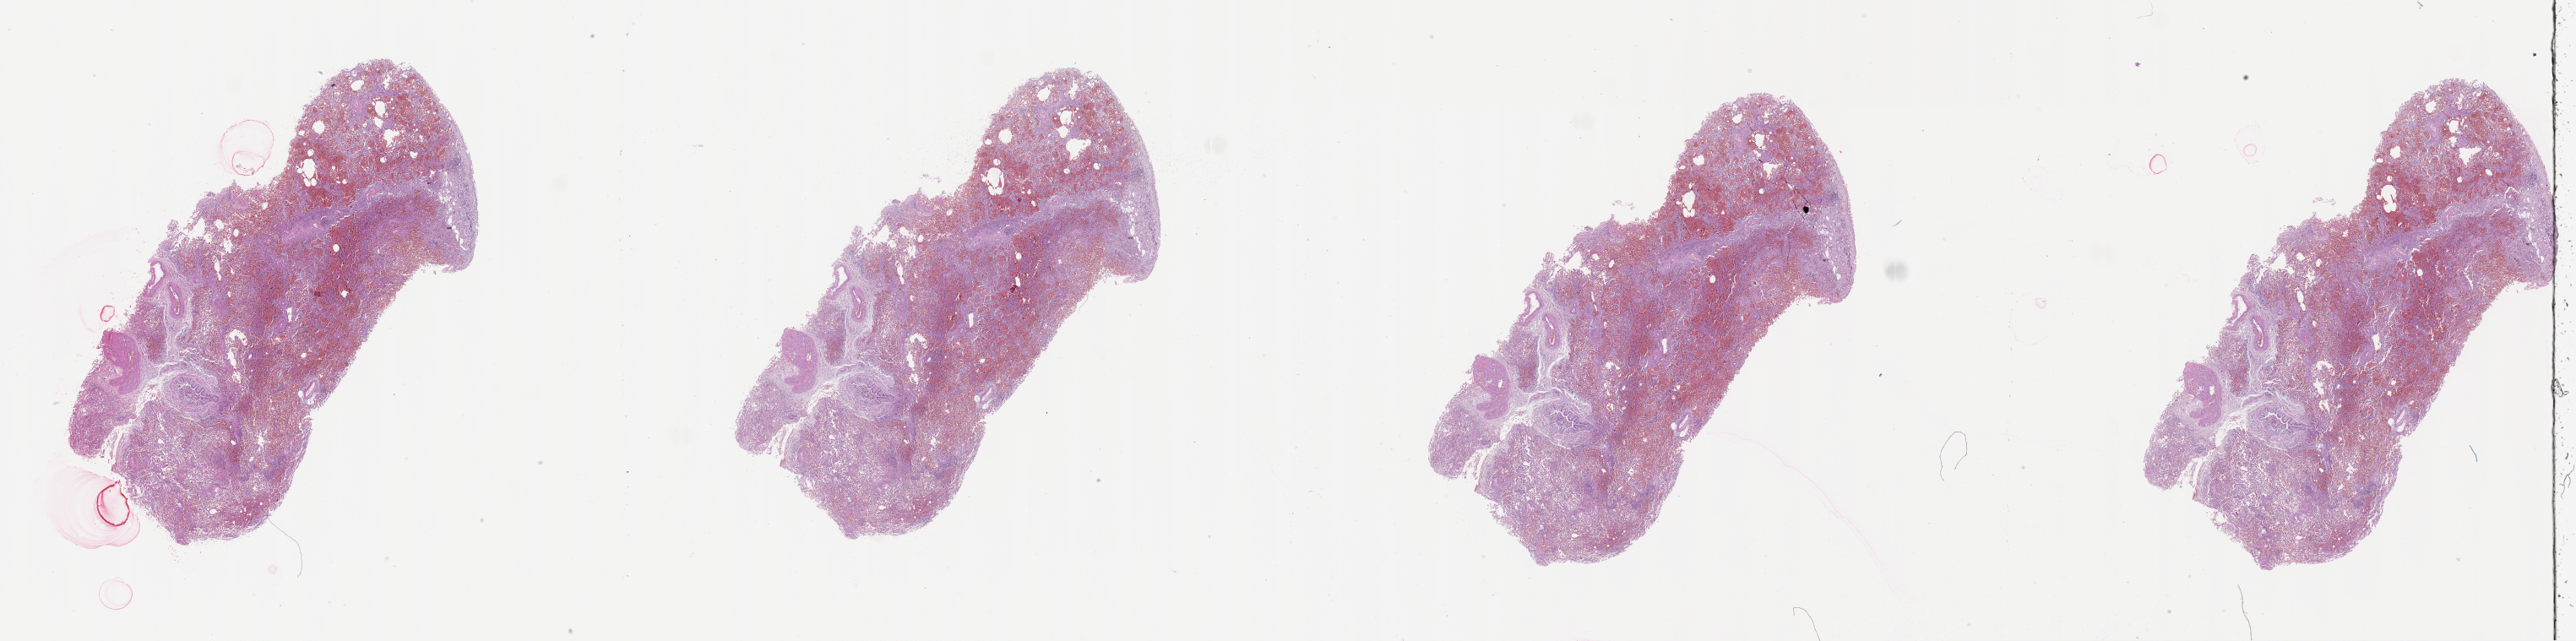
Digitized Hematoxylin and eosin (H&E) stained tissue section (whole slide) — shown as a low-resolution overview of the whole scanned area (about 49.1 x 12.2 mm); normal (non-tumour) tissue sample, lung. Patient: male, age 74 years.
This section: normal (non-tumour) tissue from the same patient. Patient diagnosis (cohort enrolment): squamous cell carcinoma (lung).